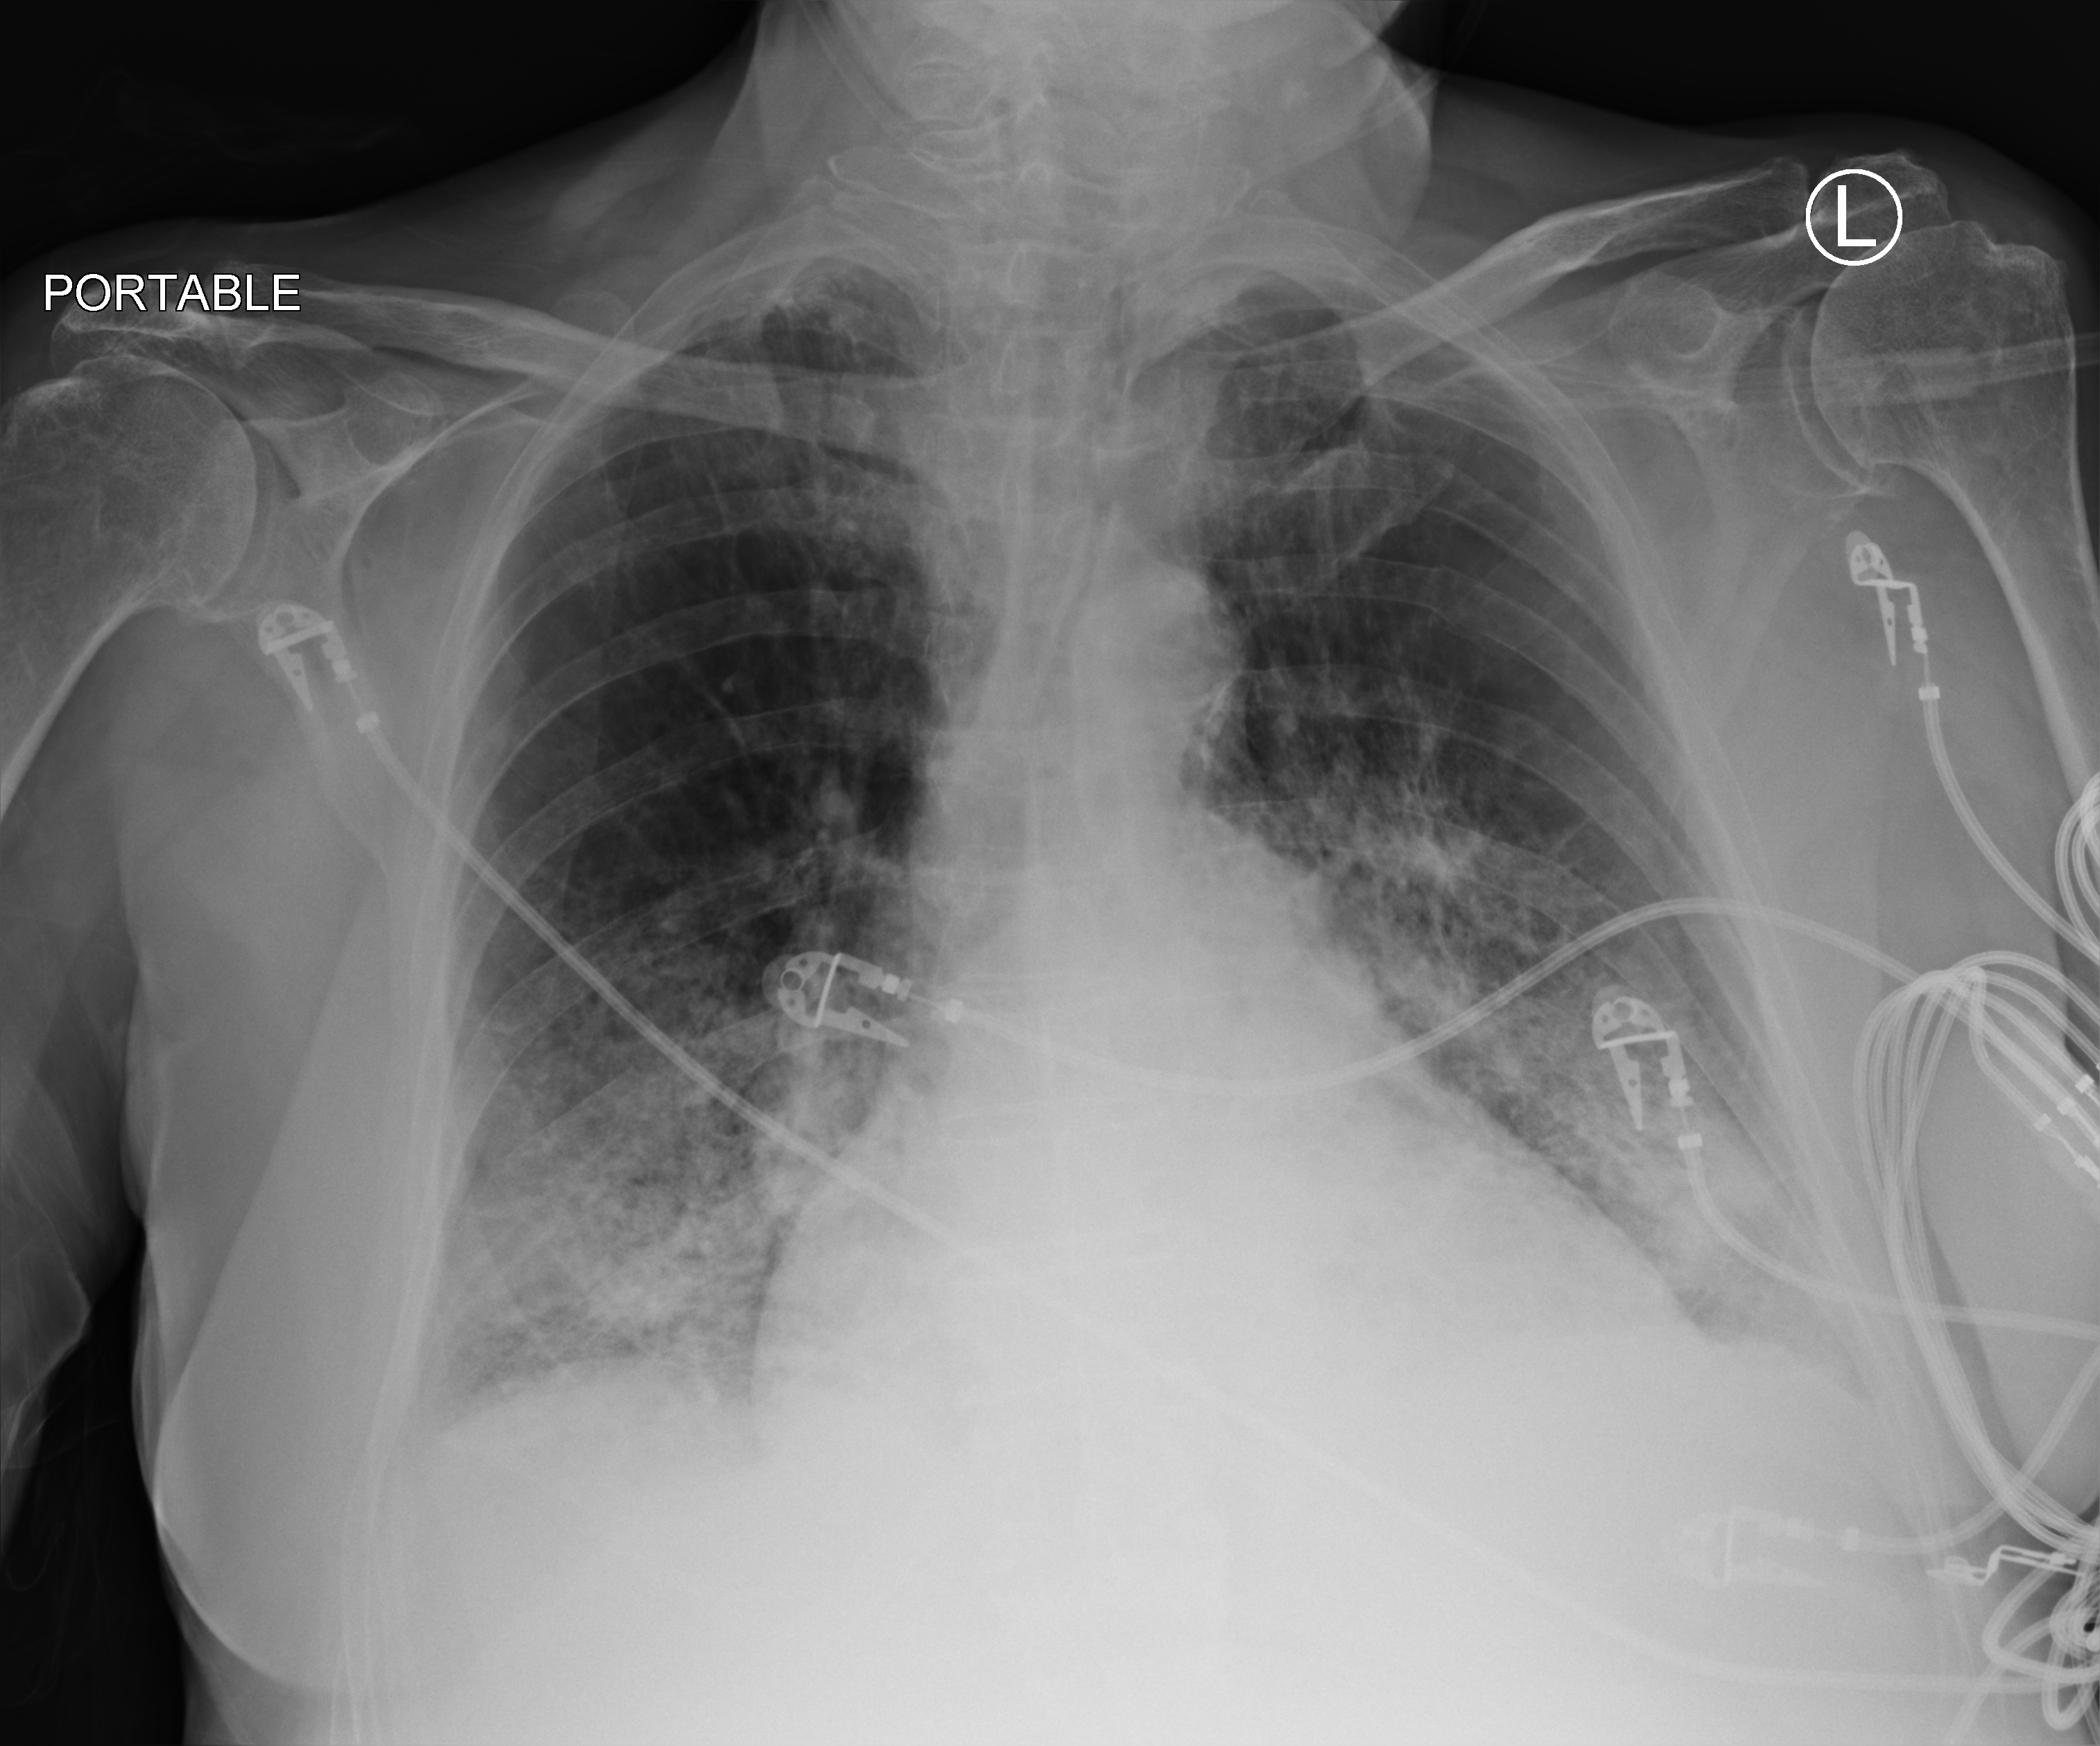
Chest X-ray (portable); anteroposterior (AP) projection. Male patient hospitalised with COVID-19, age 75–90 years.
Admission-level facts for this patient (not findings on this image; timing relative to this image not recorded):
- other chronic lung disease (admission record): no
- mechanically ventilated during this hospital stay: no
- admitted to intensive care during this hospital stay: no